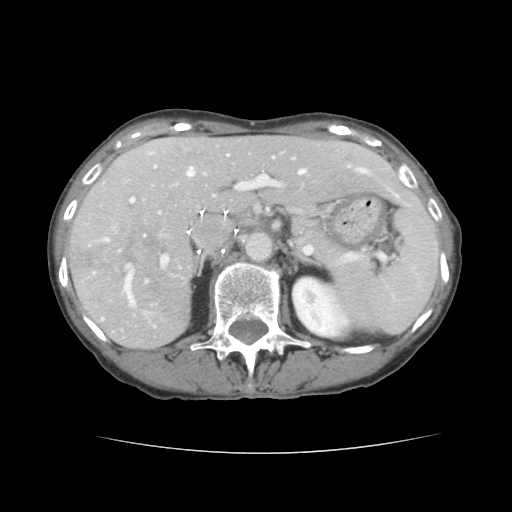
Contrast-enhanced abdominal CT, one axial slice; 120 kVp; soft-tissue window (W 400 / L 40 HU); 2.5 mm slice thickness; 512 × 512 image matrix, field of view 319 × 319 mm. Female patient, age 77 years. From the clinical record (not read from this slice): diagnosis: colorectal cancer liver metastases, imaged before liver resection; multiple liver metastases: yes; largest metastasis: 3 cm; chemotherapy before resection: yes.
Outlined on this slice (manually delineated by an expert):
- hepatic veins: bounding box [x1, y1, x2, y2] px = [150, 152, 367, 327]
- liver: [68, 136, 422, 348]
- planned liver remnant (the part of the liver to remain after resection): [153, 136, 419, 213]
- portal vein (with intrahepatic branches): [105, 158, 305, 305]
- liver metastasis: [121, 227, 169, 268]